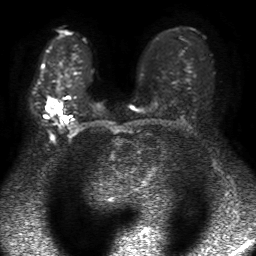
Breast MRI, one axial slice. Slice 32 of 50 in the series (ordered by position). Diffusion-weighted series; image 2 of 4 stored at this slice position (different b-values; order by instance number). 1.5 T. 4 mm slice thickness. 256 × 256 image matrix, field of view 320 × 320 mm. Female patient.
Structures marked on this image (manually delineated by an expert):
- tumour on diffusion-weighted imaging: bounding box <46,97,58,111> (left, top, right, bottom; pixels)